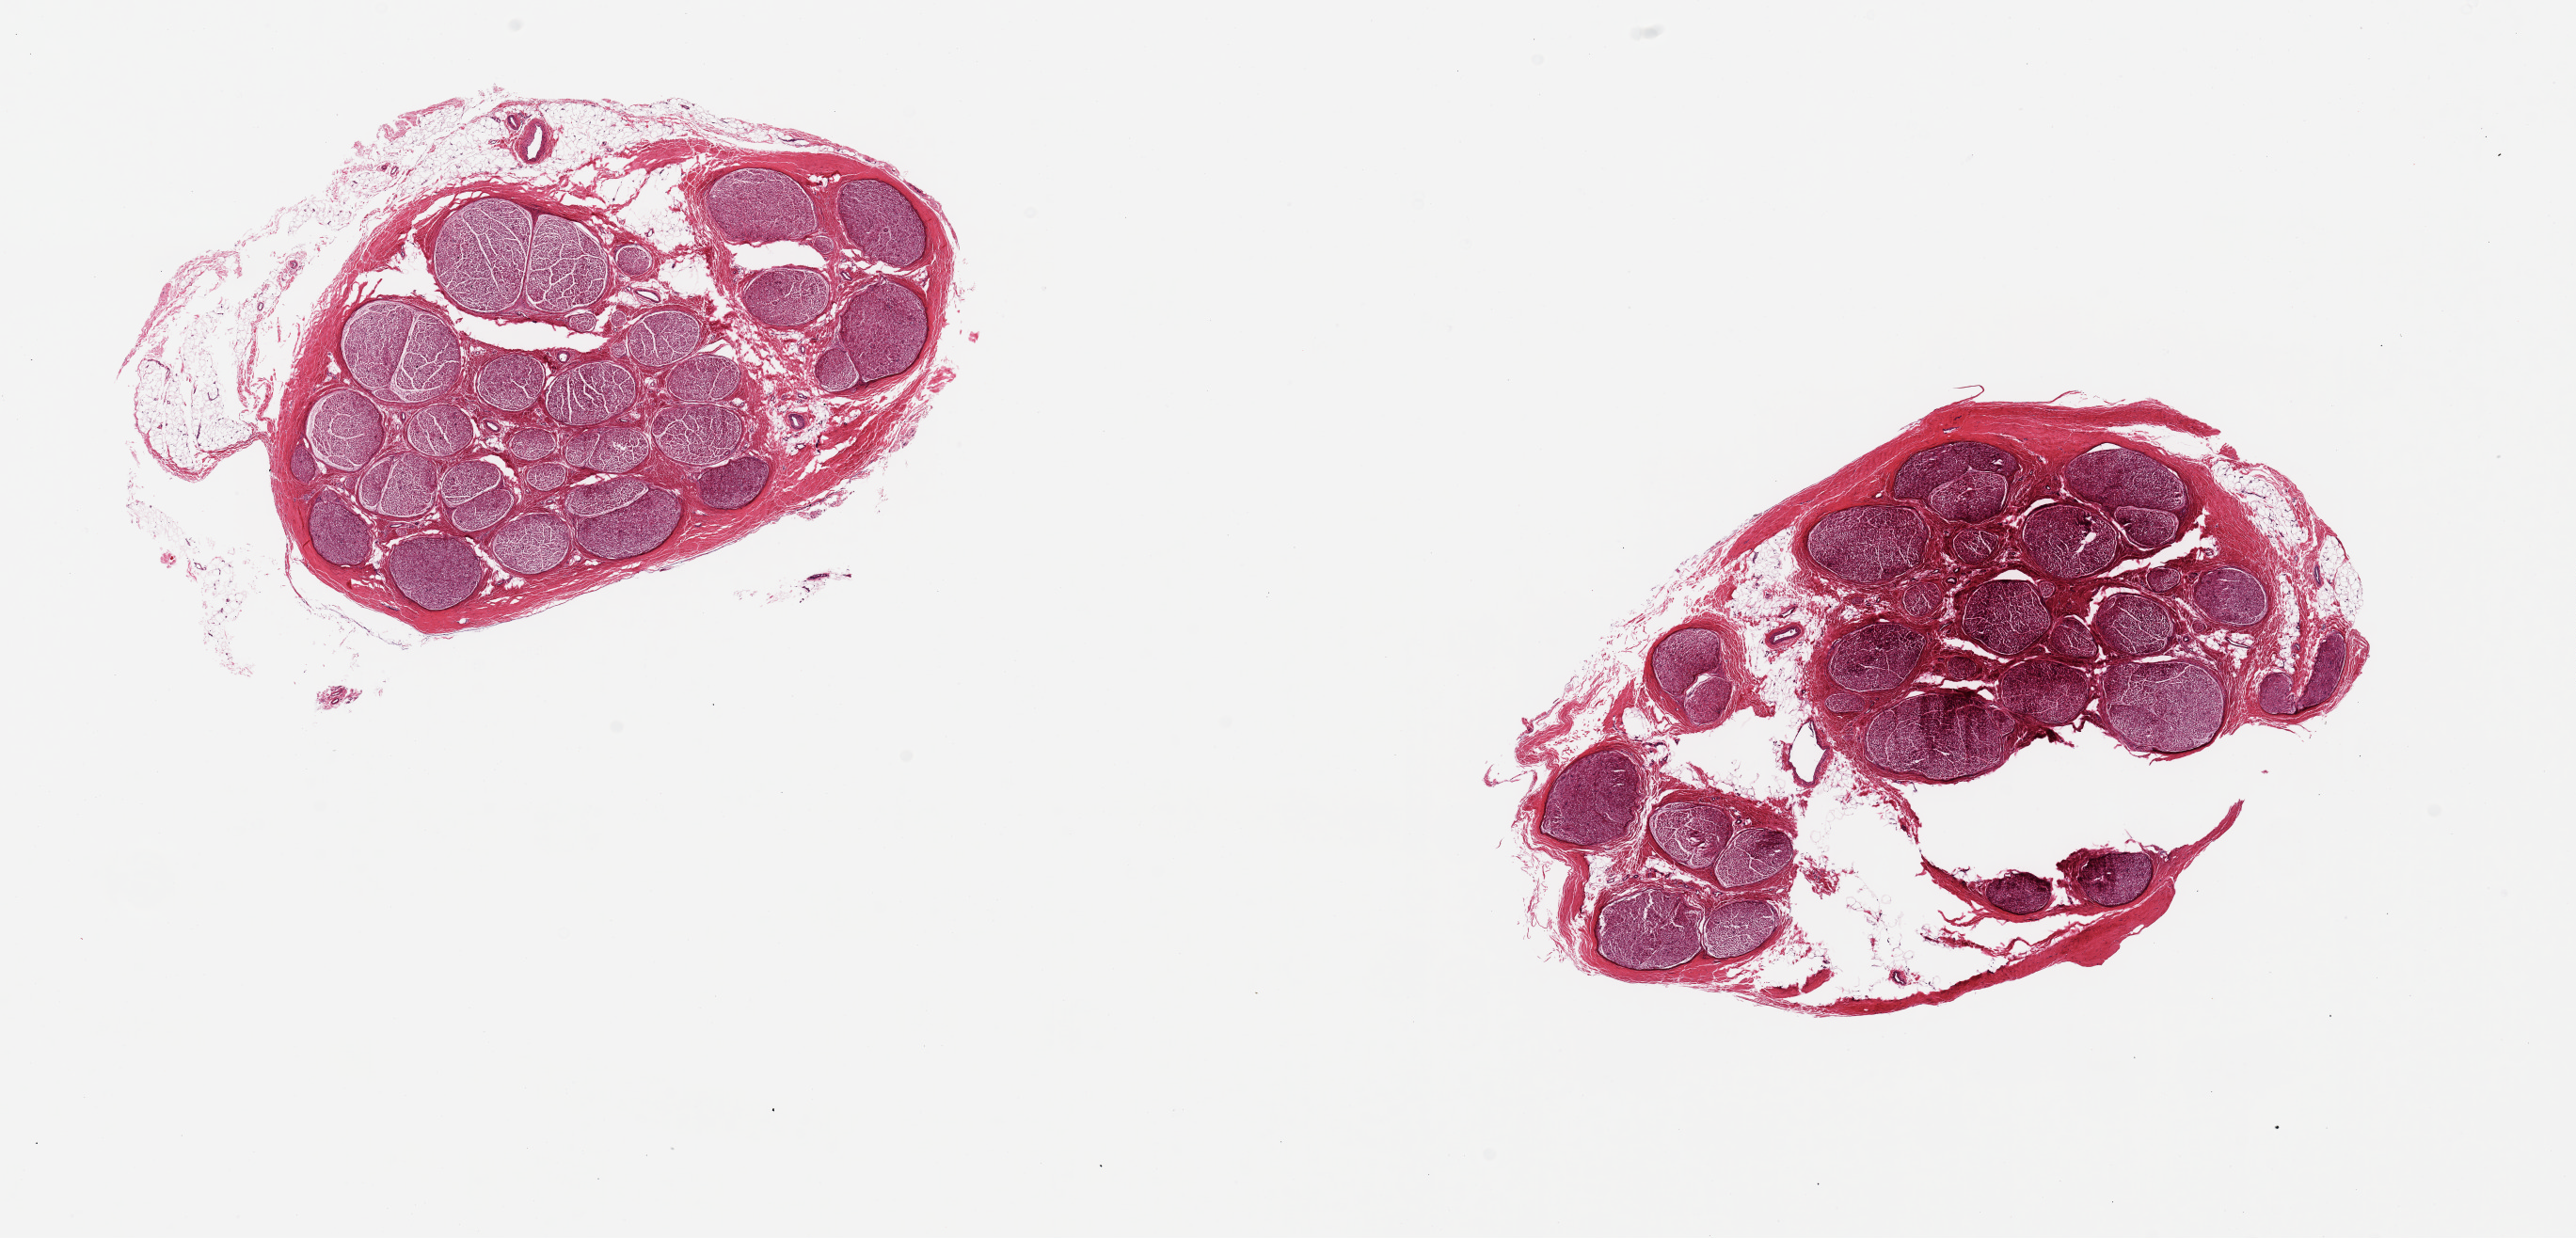
Digitized haematoxylin and eosin-stained section, whole scanned area (about 21.7 x 10.4 mm, slide scanned at 20x) shown as a low-resolution overview. PAXgene-fixed paraffin-embedded (PFPE) section. Target tissue: tibial nerve. Donor tissue sample. Male donor.
Reviewer comment on this tissue sample: 2 pieces ~4mm d. Patchy nubbins of adherent fat, ~0.5mm noted on one.